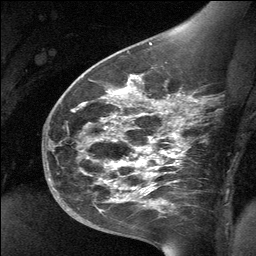
Breast MRI (dynamic contrast-enhanced), one sagittal slice; slice 41 of 64 in the series (ordered by position); dynamic contrast-enhanced study with each time point stored as its own series, time point 2 of 3 at this slice position (early post-contrast, ordered by acquisition time); 1.5 T; TE 4.8 ms, TR 27 ms; 2 mm slice thickness; 256 × 256 image matrix. Female patient, age 39 years. From the clinical record (not read from this slice): setting: breast cancer imaged before/during neoadjuvant chemotherapy; receptor status: HER2-positive.
Outlined on this slice (semi-automatic segmentation, software-assisted and operator-edited):
- analysis volume of interest (the breast-tissue region the enhancement analysis was run in; not a lesion): bounding box [x1, y1, x2, y2] px = [70, 69, 198, 224]
- tumour enhancement mask (voxels above the 90 % enhancement threshold inside the analysis volume of interest): [119, 76, 174, 192]